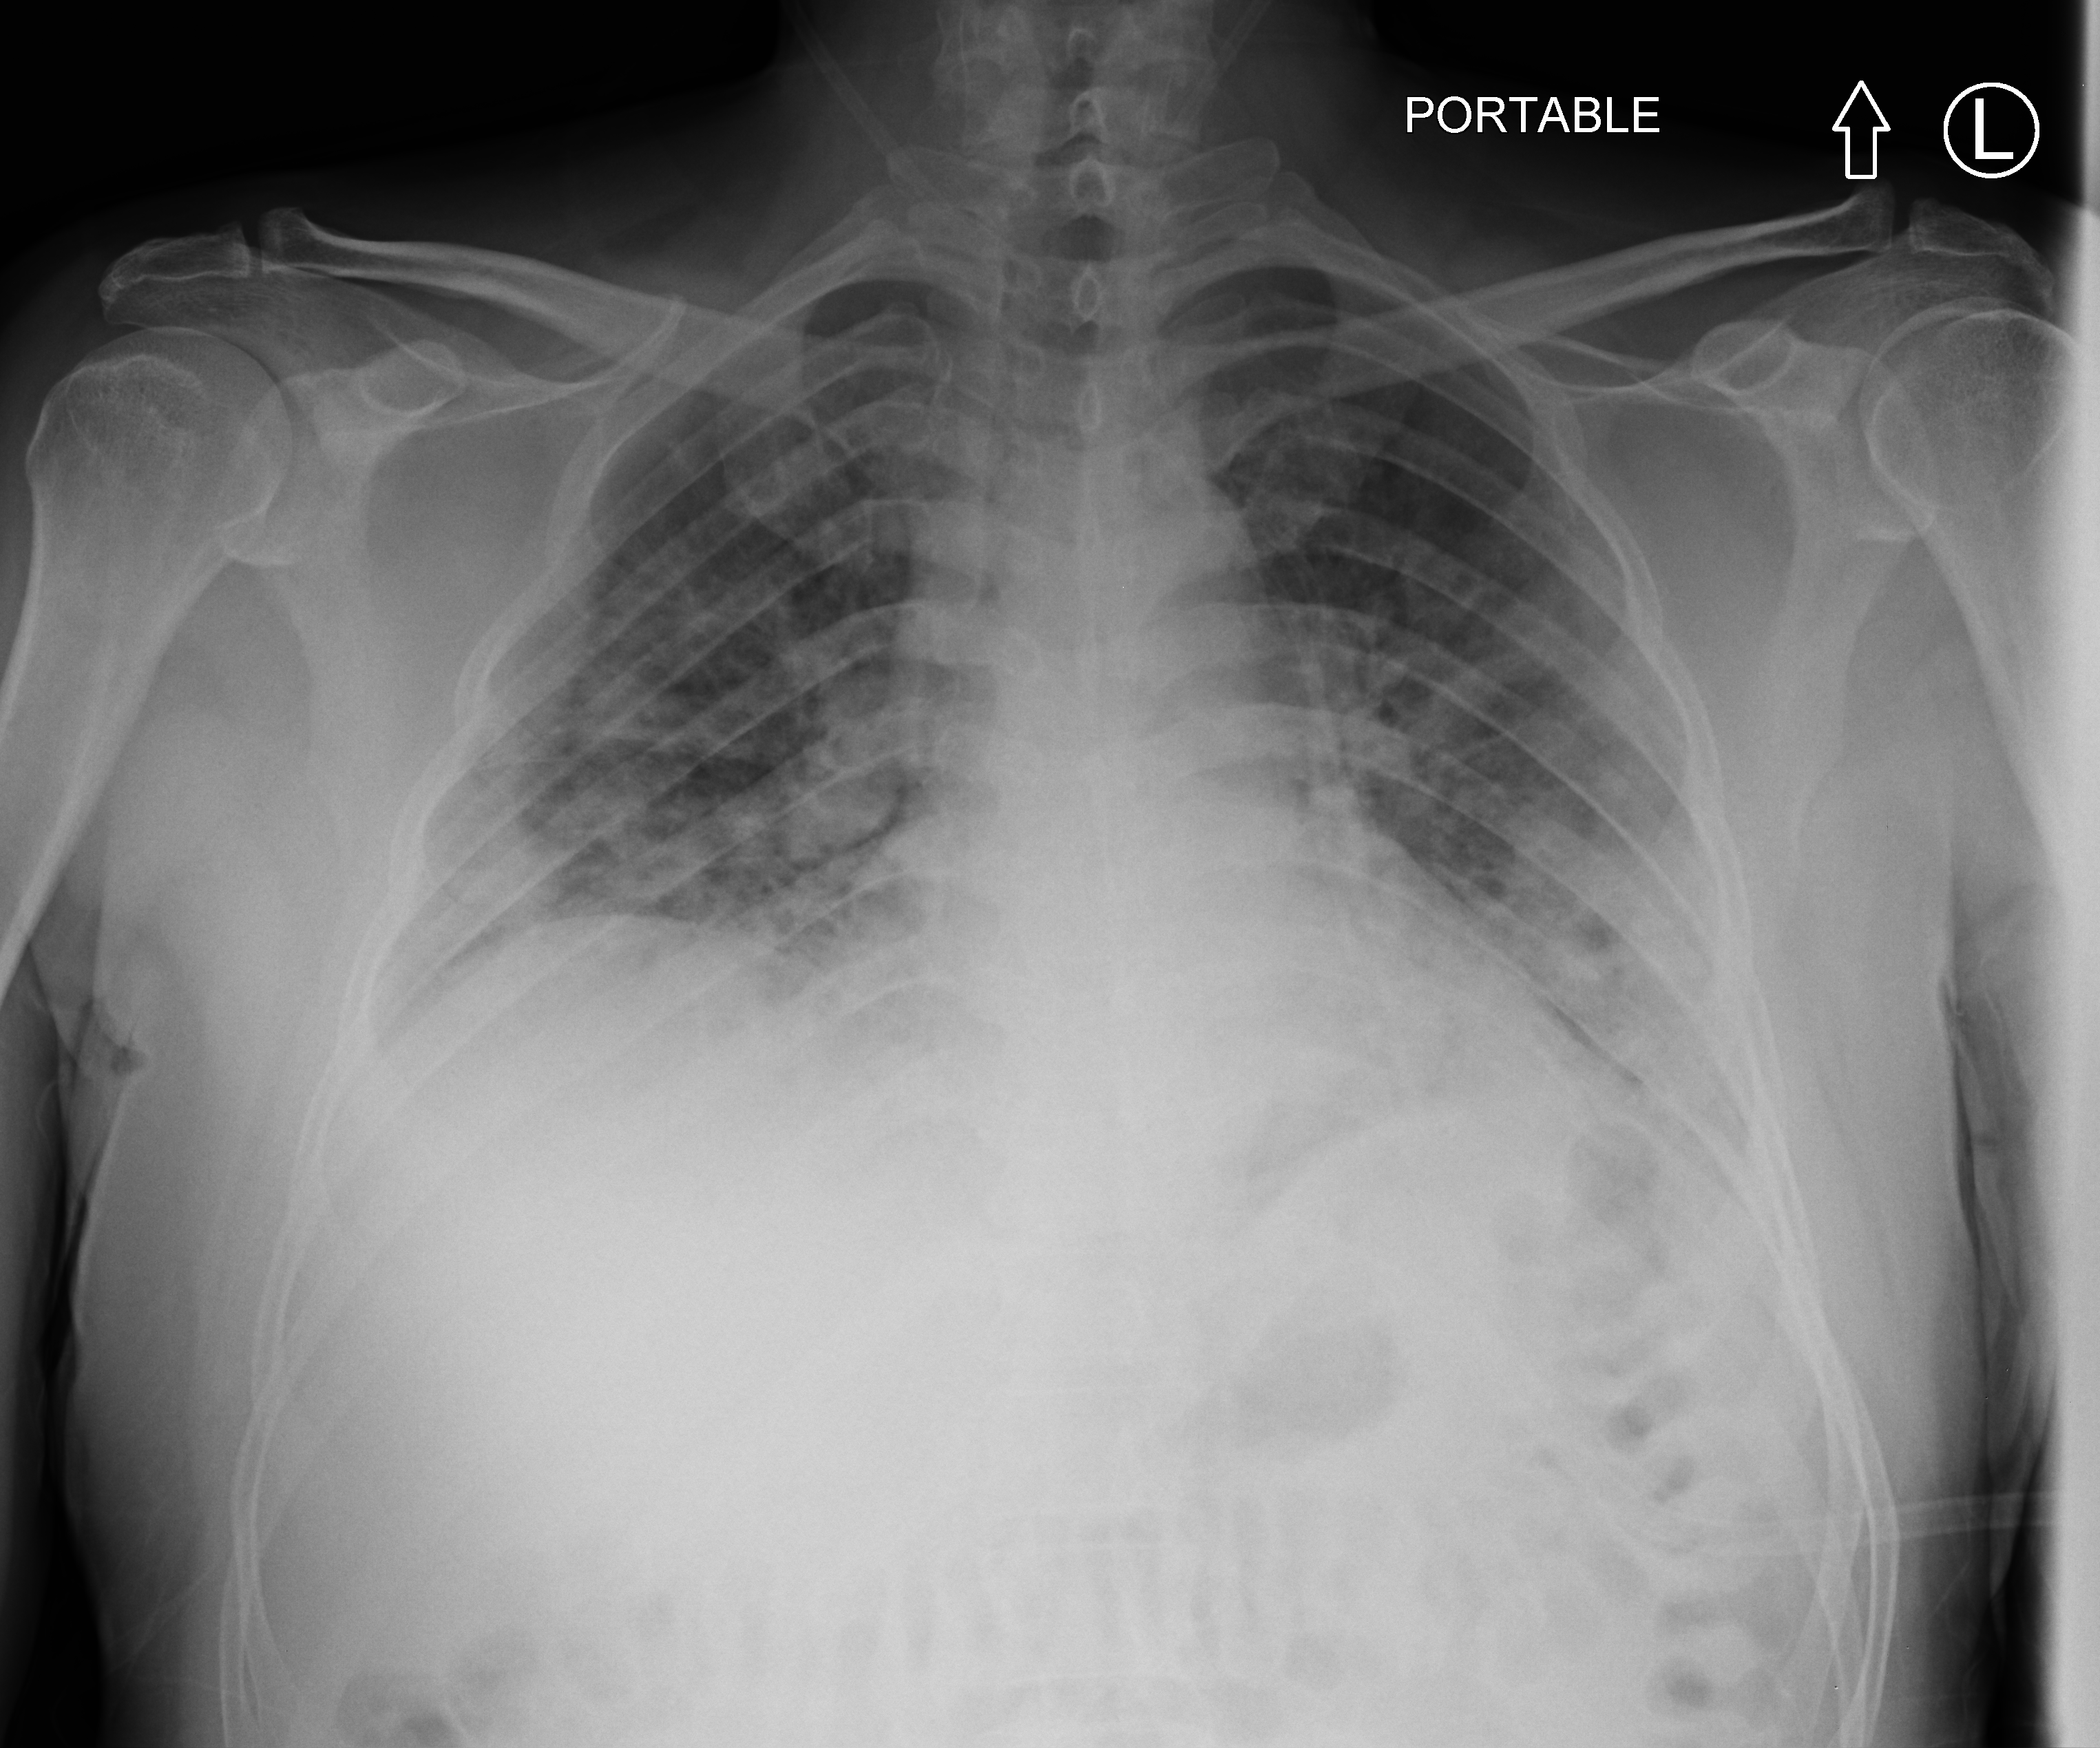
Bedside chest radiograph (computed radiography); anteroposterior (AP) projection. Patient hospitalised with COVID-19; male, aged 18–59 years.
From the hospital-stay record, not from the radiograph (when in the stay this image was taken is not recorded): admitted to intensive care during this hospital stay: no.